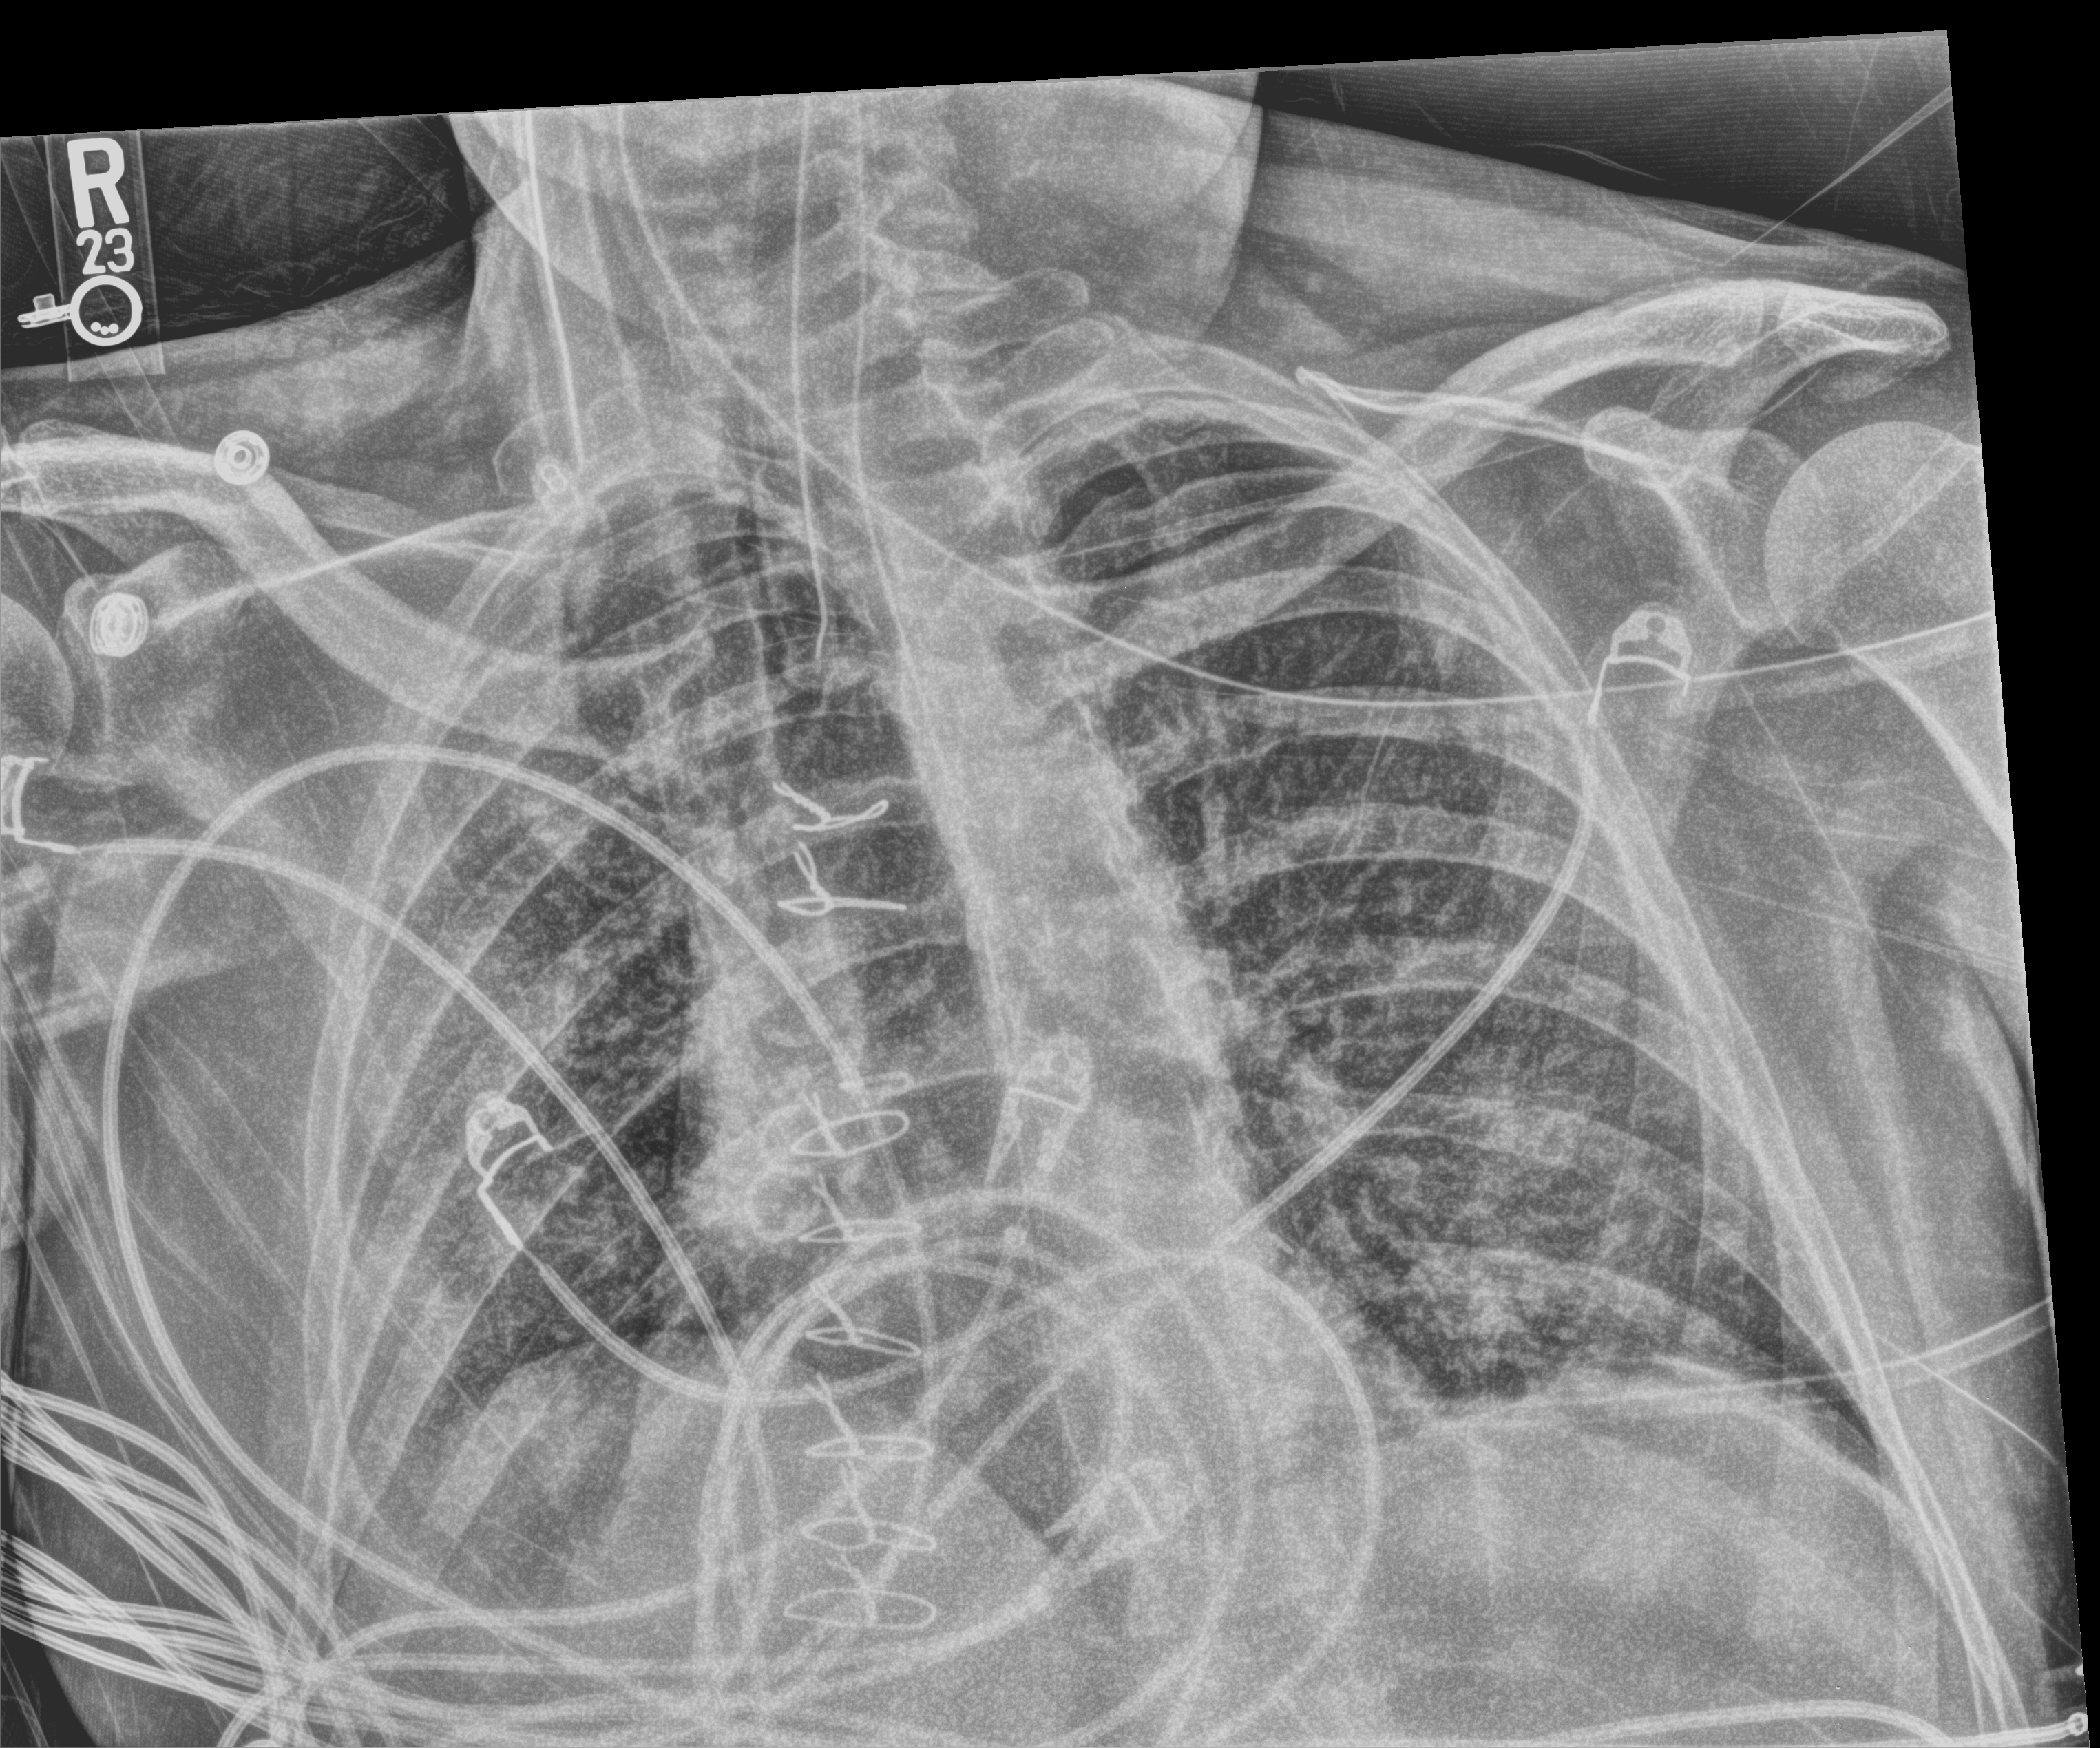
Bedside chest radiograph (computed radiography), anteroposterior (AP) projection. Male patient hospitalised with COVID-19, age 18–59 years.
From the hospital-stay record, not from the radiograph (when in the stay this image was taken is not recorded): admitted to intensive care during this hospital stay: yes.